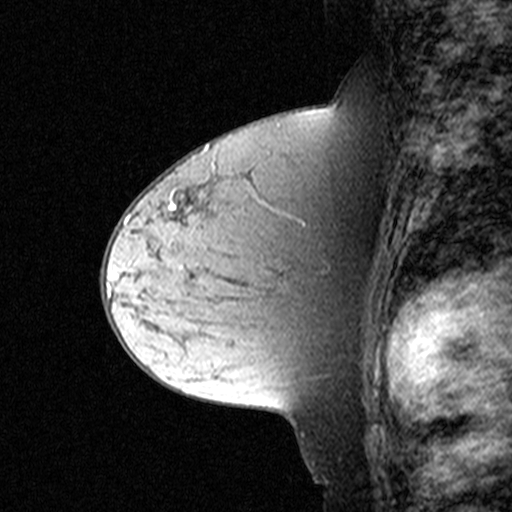
Breast MRI (dynamic contrast-enhanced), one sagittal slice; slice 22 of 44 in the series (ordered by position); dynamic contrast-enhanced study with each time point stored as its own series, time point 2 of 3 at this slice position (early post-contrast, ordered by acquisition time); 1.5 T; TE 4.5 ms, TR 11 ms; 3 mm slice thickness; 512 × 512 image matrix. Patient: female, 44 years. From the clinical record (not read from this slice): setting: breast cancer imaged before/during neoadjuvant chemotherapy; receptor status: triple-negative.
Structures marked on this image (semi-automatic segmentation, software-assisted and operator-edited):
- analysis volume of interest (the breast-tissue region the enhancement analysis was run in; not a lesion): bounding box <174,204,303,305> (left, top, right, bottom; pixels)
- tumour enhancement mask (voxels above the 90 % enhancement threshold inside the analysis volume of interest): <174,204,176,210>